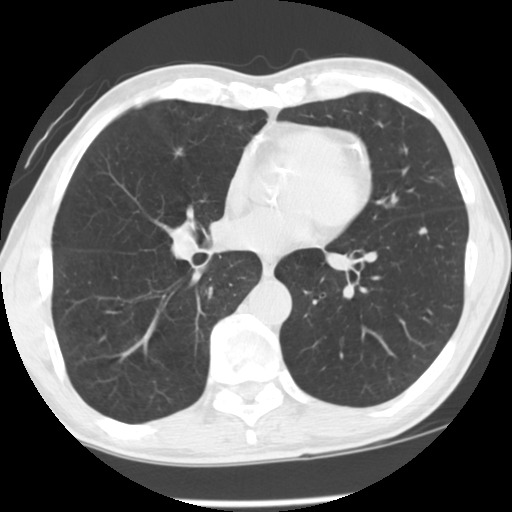
Low-dose screening chest CT, one axial slice. Position 62 of 139 along the scan axis. Reconstruction kernel STANDARD. 120 kVp. Lung window (W 1500 / L -600 HU). 512 × 512 image matrix, field of view 320 × 320 mm.
Annotated regions visible in this slice (outlined manually by an expert reader):
- lesion 1 (tumor, lower lobe of left lung): bounding box [x1, y1, x2, y2] px = [420, 228, 426, 234]